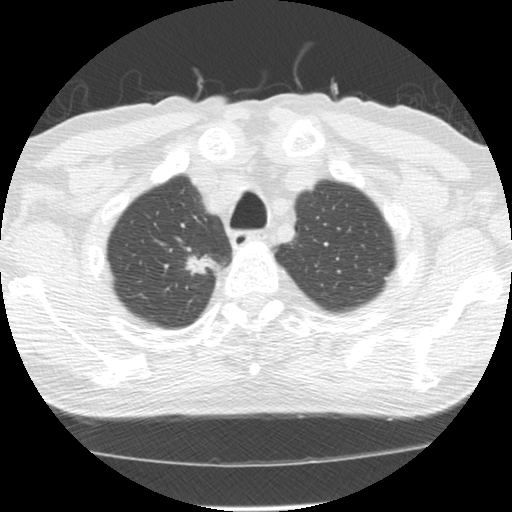
Axial slice from a low-dose chest CT screening exam; first (baseline) screen; lung window (W 1500 / L -600 HU); slice 25 of 139 in the series; 512 × 512 image matrix. Male, age 64 years at enrolment.
- Expert-annotated lung lesion, bounding box <178,239,224,280> (left, top, right, bottom; pixels).
- Reader record for this screening exam (exam-level; its link to the box is not recorded): non-calcified nodule or mass ≥4 mm, right upper lobe, 20 × 13 mm, spiculated (stellate) margins, soft tissue attenuation.
- Official screen result: positive, change unspecified: nodule(s) >= 4 mm or enlarging nodule(s), mass(es), or other non-specific abnormalities suspicious for lung cancer.
- Participant outcome: lung cancer diagnosed 73 days after this screen — adenocarcinoma, NOS, right upper lobe, moderately differentiated (G2), stage IA (AJCC 6th edition), 17 mm at pathology.